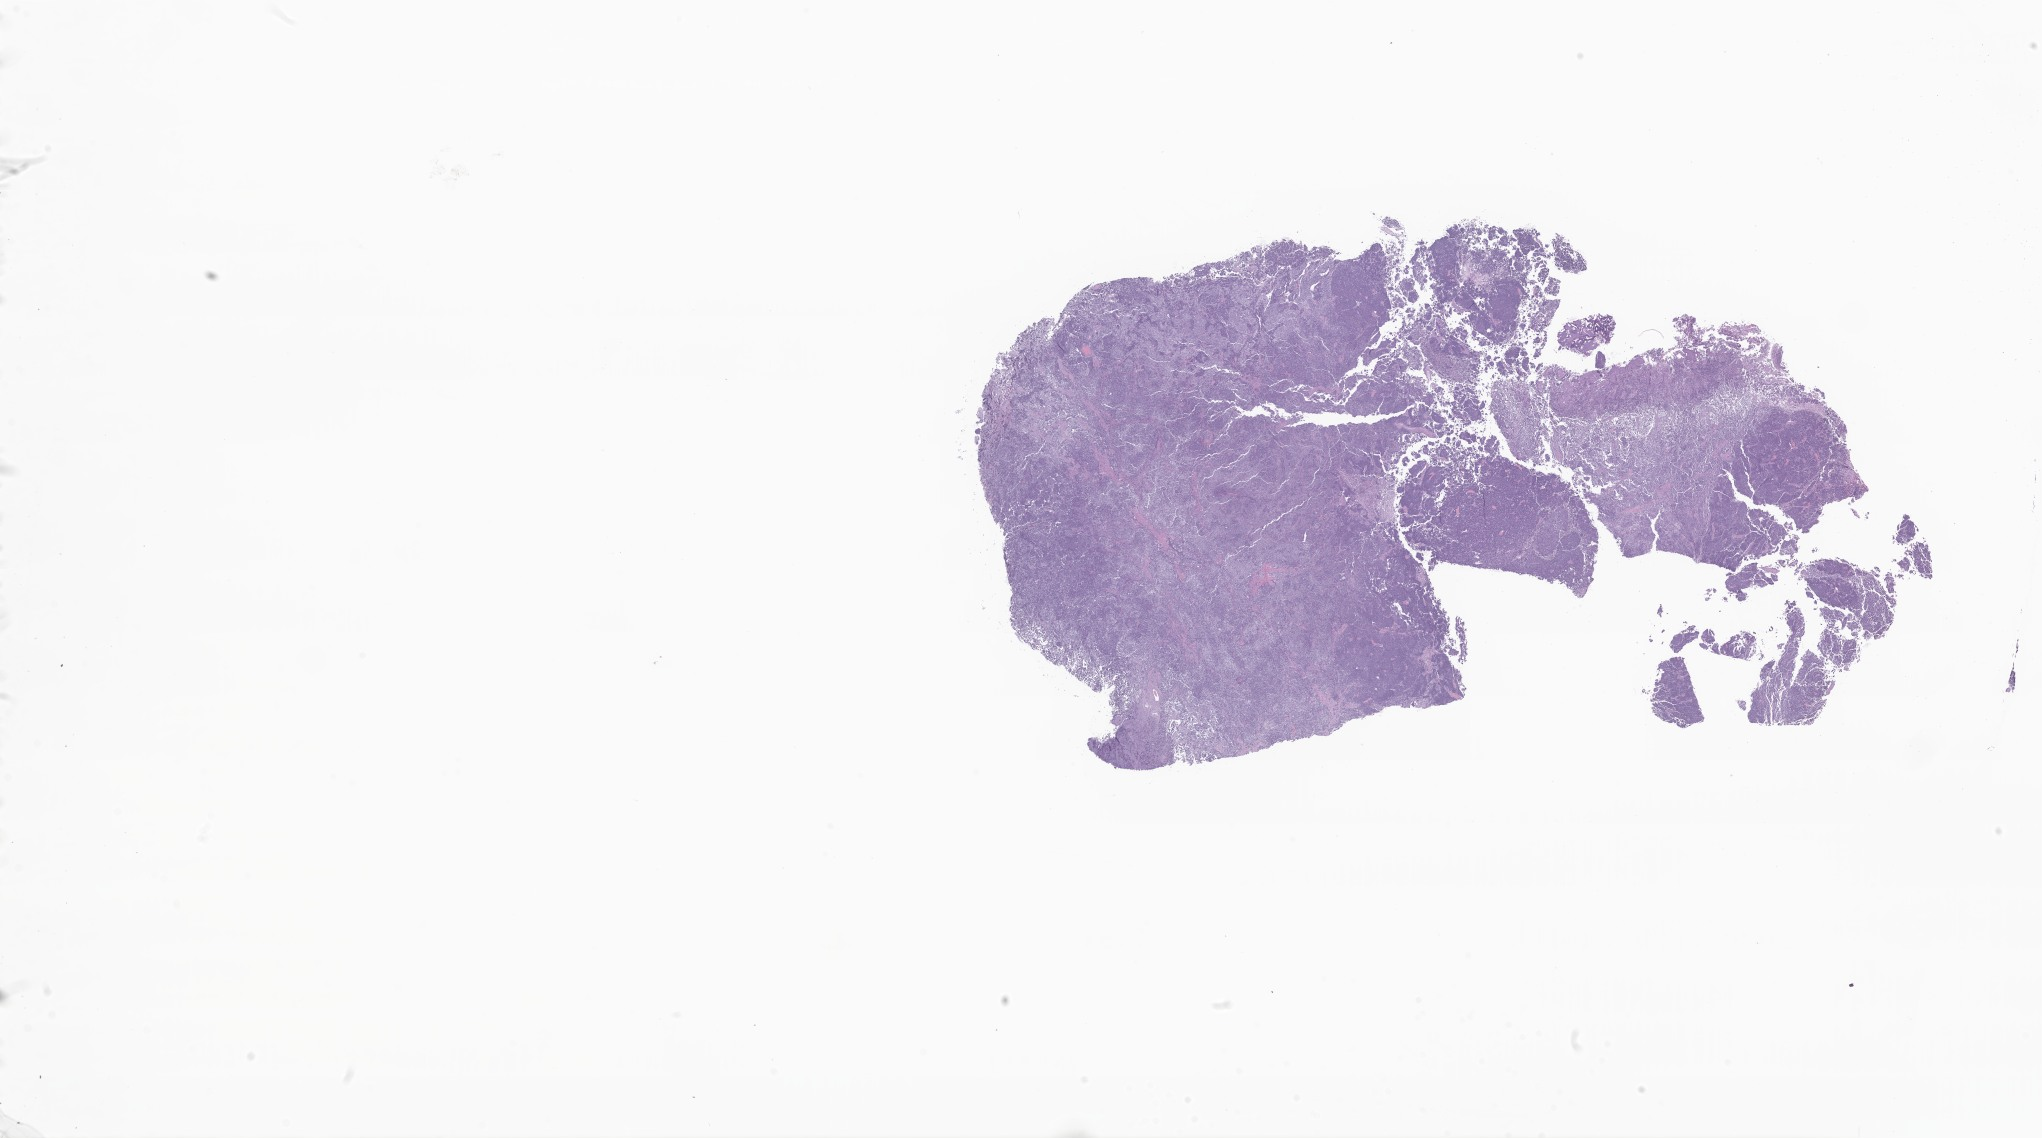
H&E whole-slide image of tumor tissue from the brain — a low-resolution overview of the entire scanned area, about 34.4 x 19.2 mm, formalin-fixed paraffin-embedded section. Patient male; age 38 months (3 years 2 months).
Diagnosis (ICD-O-3 morphology term): Medulloblastoma, NOS.